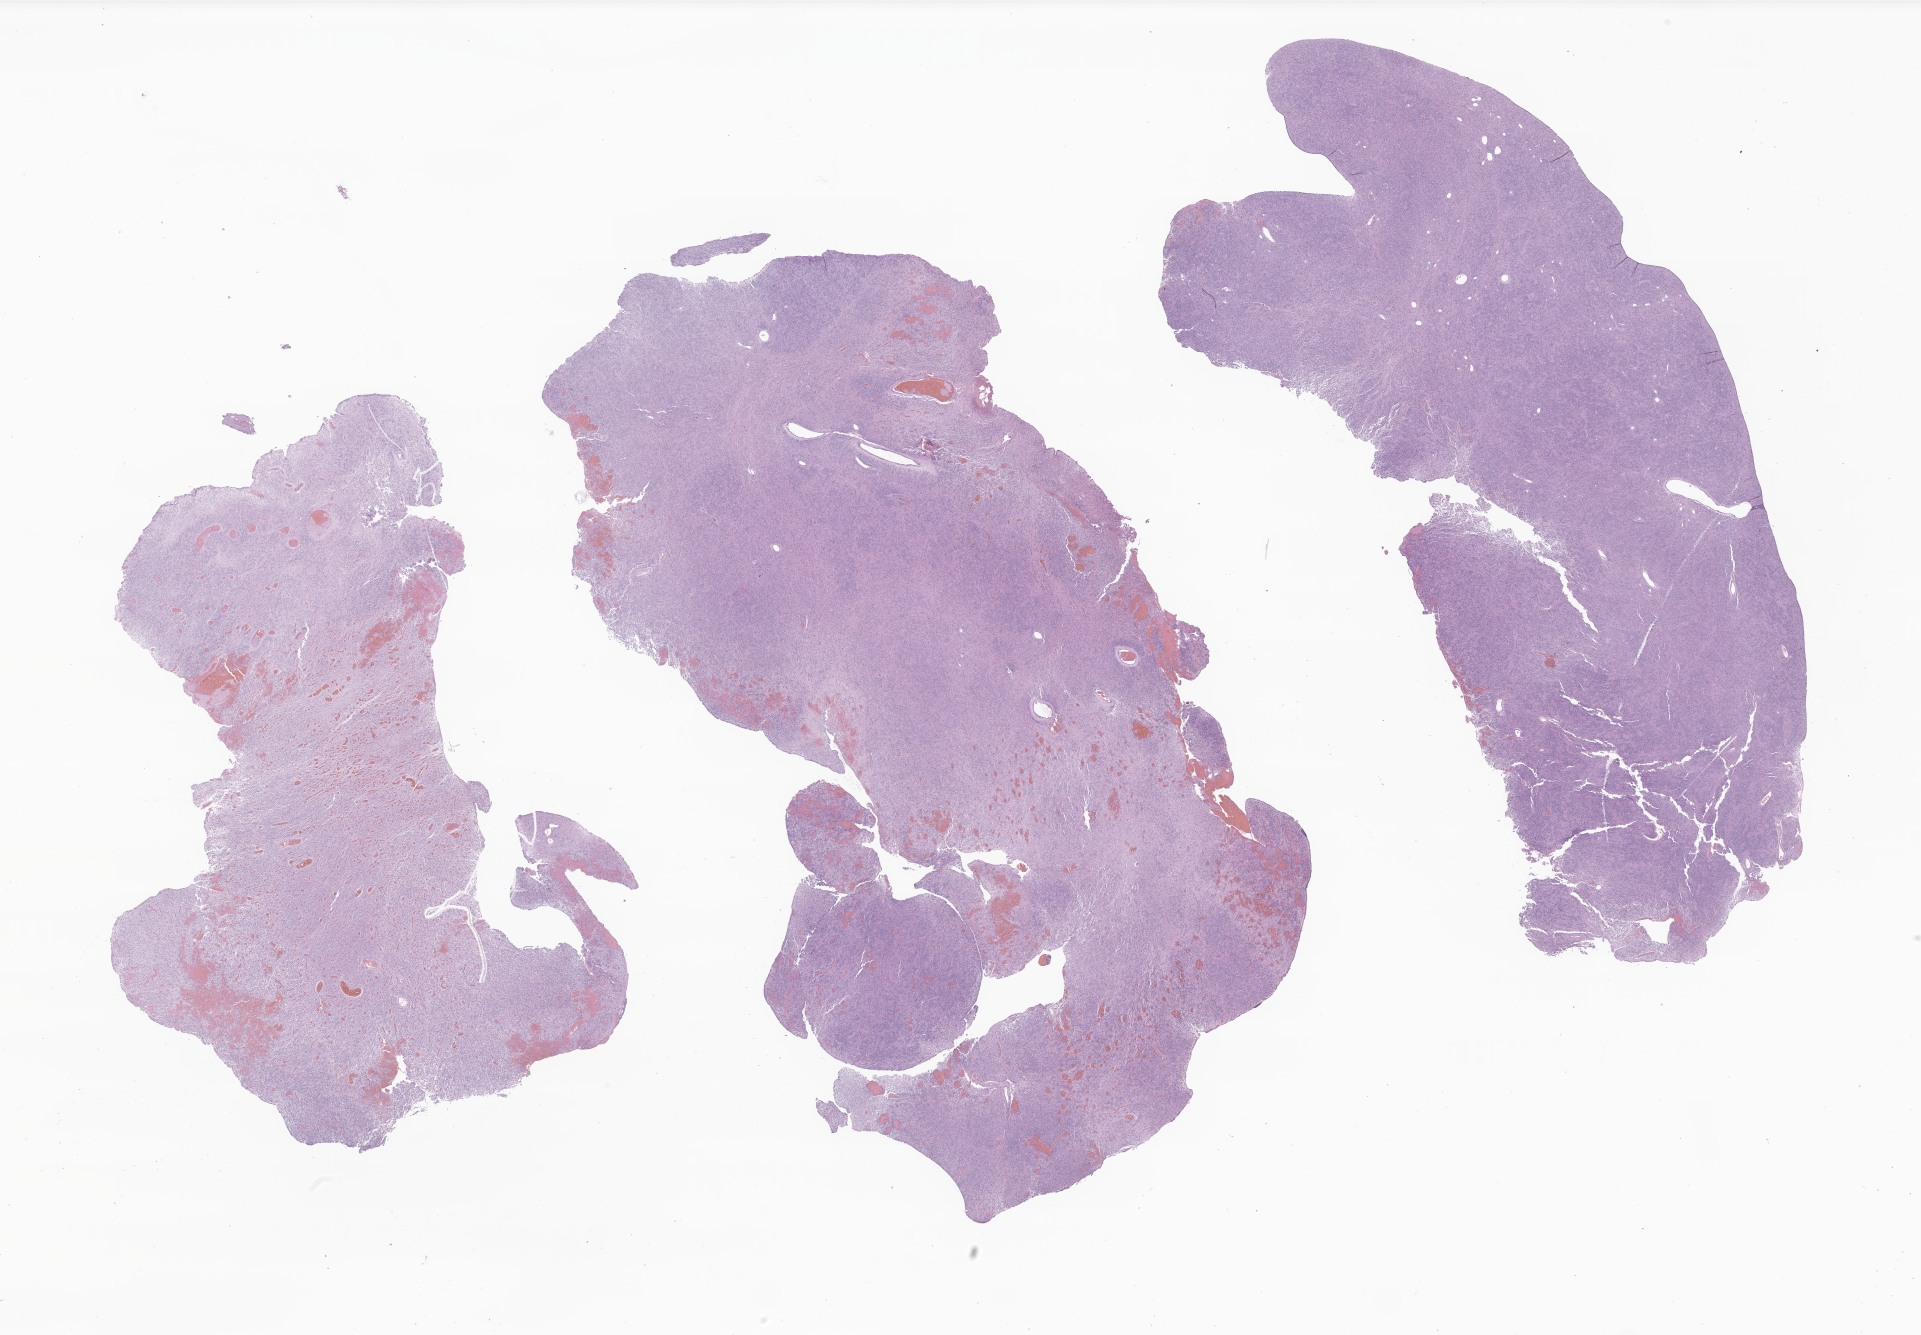
Hematoxylin and eosin (H&E) whole-slide image of tumor tissue from the cerebral ventricle, whole scanned area (about 32.4 x 22.5 mm) shown as a low-resolution overview; formalin-fixed, paraffin-embedded (FFPE) tissue. Patient: male, age 473 days (about 1.3 years).
- diagnosis (ICD-O-3 morphology term): Neoplasm, malignant